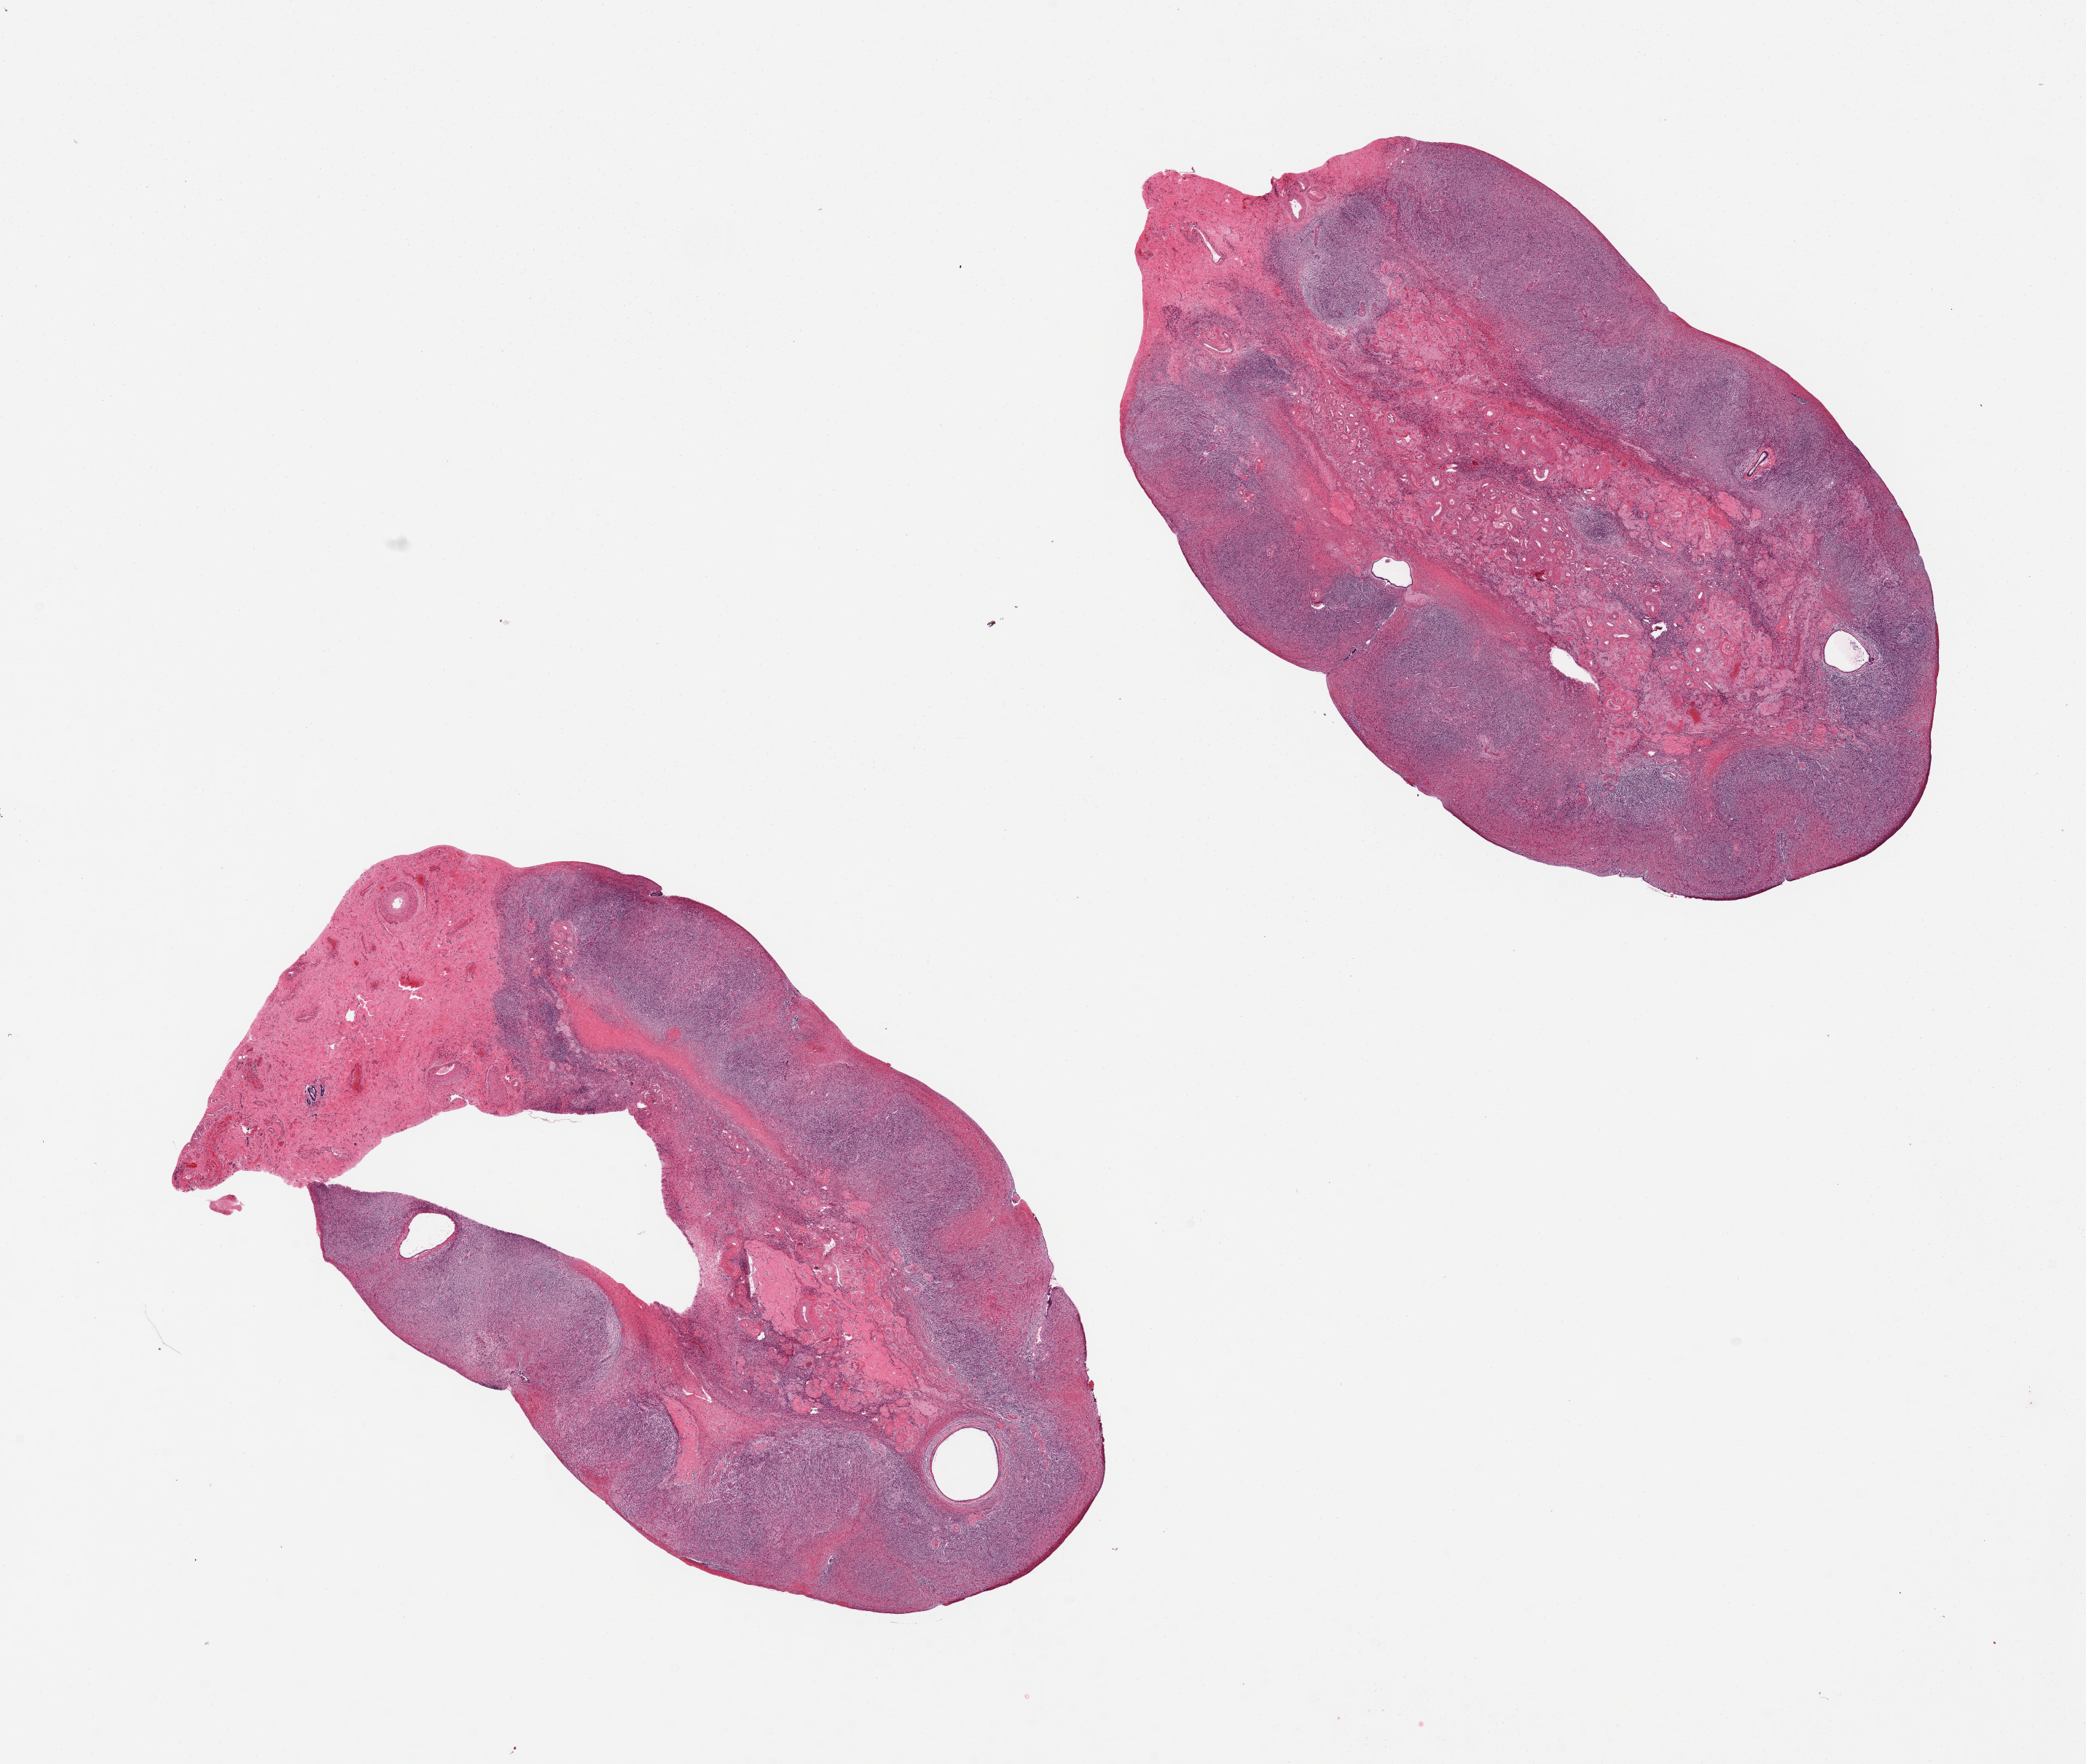
H&E whole-slide image — shown as a low-resolution overview of the whole scanned area (about 22.6 x 19.1 mm, slide scanned at 20x), PAXgene-fixed, paraffin-embedded tissue, target tissue: ovary, tissue donor sample. Donor sex: female.
Pathologist's review note for this sample: 2 pieces, post menopausal involution/atrophy, prominent hilar vessels.